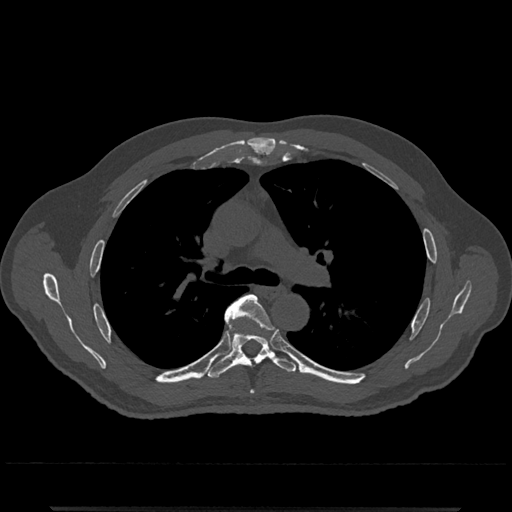
CT including the spine, one axial slice. Position 793 of 797 along the scan axis. 120 kVp. Bone window (W 1800 / L 400 HU). 512 × 512 image matrix, field of view 393 × 393 mm. Male patient, age 67 years. Case-level facts recorded for this patient, not image findings: primary cancer: prostate.
Annotated regions visible in this slice (semi-automatic segmentation, software-assisted and operator-edited):
- T5 vertebra: bounding box [x1, y1, x2, y2] px = [225, 294, 269, 326]
- T6 vertebra: [206, 302, 297, 379]